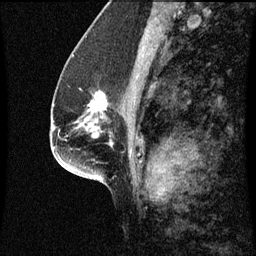
Breast MRI (dynamic contrast-enhanced), one sagittal slice. Slice 30 of 60 in the series (ordered by position). Dynamic contrast-enhanced series, image 2 of 3 at this slice position (ordered by acquisition). 1.5 T. TE 4.2 ms, TR 8.9 ms. 2 mm slice thickness. 256 × 256 image matrix, field of view 200 × 200 mm. Female patient, age 57 years. Case-level facts recorded for this patient, not image findings: setting: breast cancer imaged before/during neoadjuvant chemotherapy; receptor status: HR-positive, HER2-negative.
Annotated regions visible in this slice (semi-automatic segmentation, software-assisted and operator-edited):
- analysis volume of interest (the breast-tissue region the enhancement analysis was run in; not a lesion): bounding box <82,90,124,125> (left, top, right, bottom; pixels)
- tumour enhancement mask (voxels above the 70 % enhancement threshold inside the analysis volume of interest): <97,92,105,101>